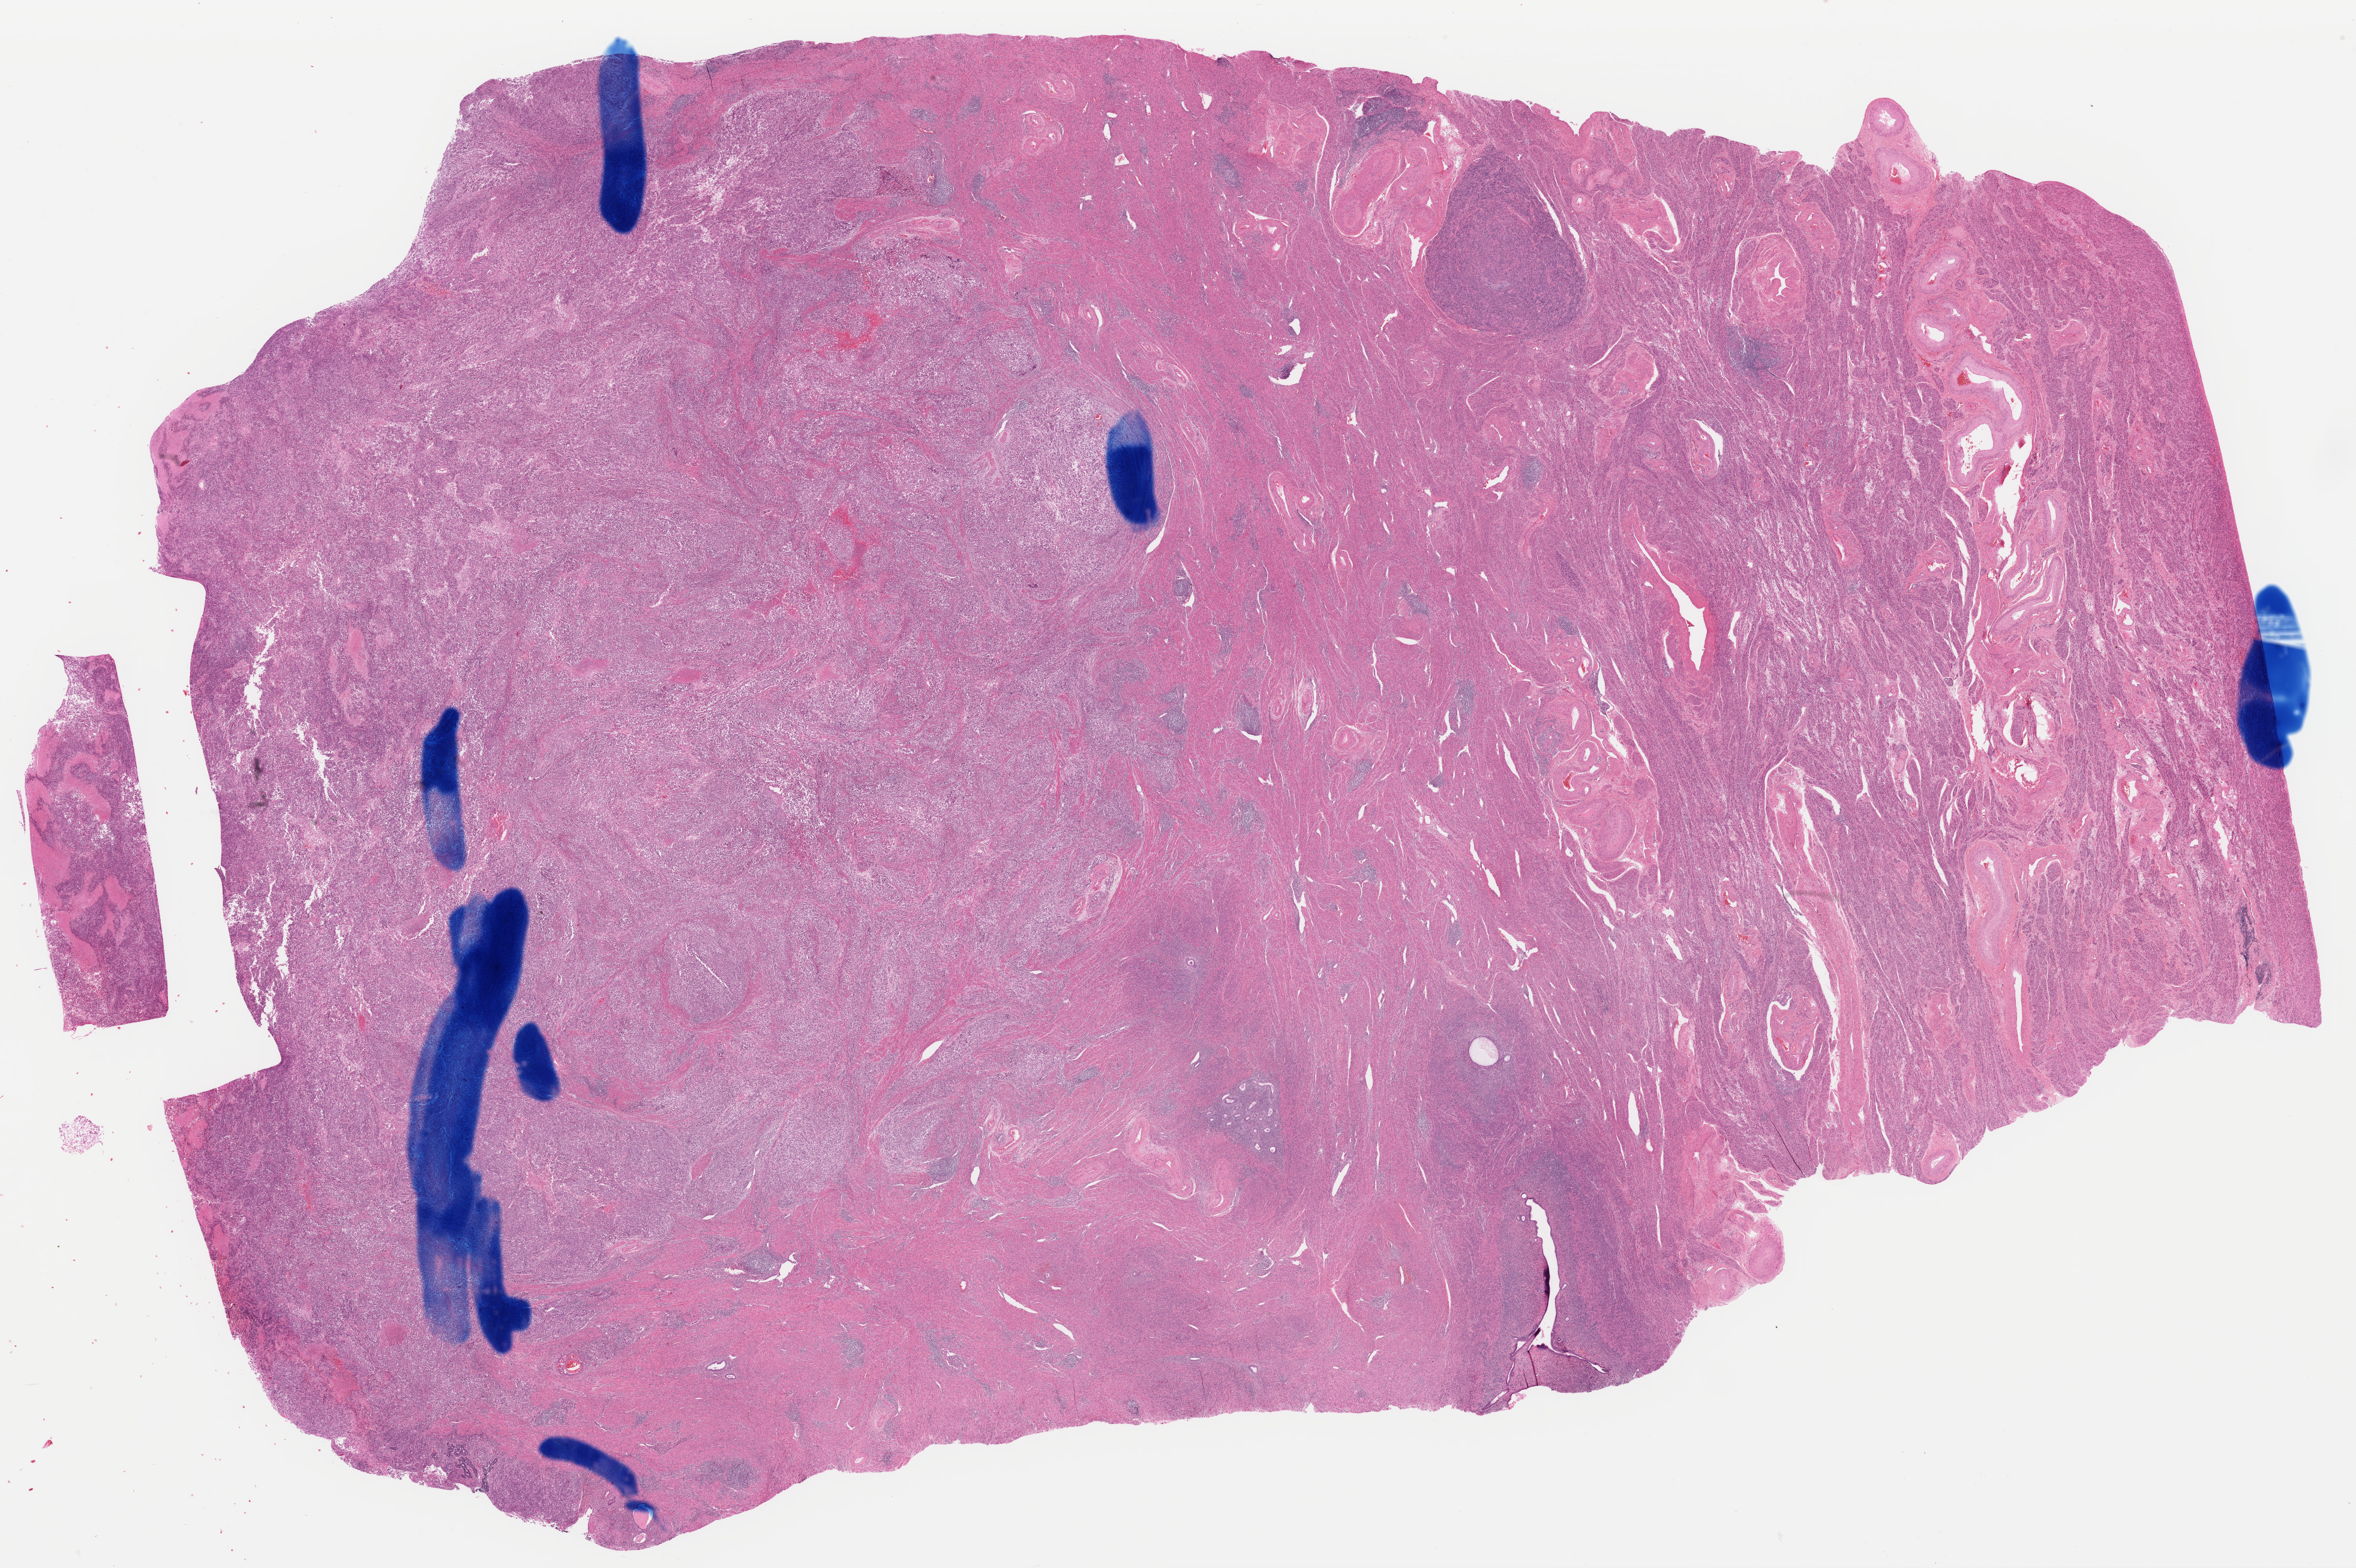
H&E whole-slide image, shown as a low-resolution overview of the whole scanned area (about 31.0 x 20.6 mm), formalin-fixed paraffin-embedded (FFPE) diagnostic section, sample: primary tumour, uterus. Female patient; age at initial diagnosis 68 years. Histologic grade: G3 (poorly differentiated).
• FIGO stage: IA
• diagnosis: Serous cystadenocarcinoma, NOS (endometrium)